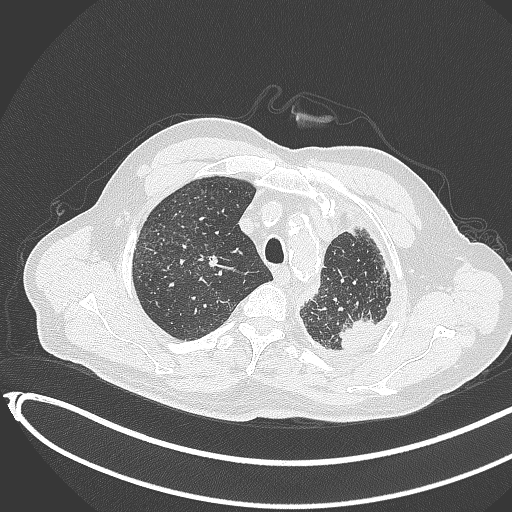
Chest CT, one axial slice; position 353 of 451 along the scan axis; reconstruction kernel B70f; 120 kVp; lung window (W 1500 / L -600 HU); 512 × 512 image matrix. Patient: male, 78 years. Case-level facts recorded for this patient, not image findings: clinical TNM (as recorded): T1c N0 M1.
Structures marked on this image (rectangle marked by the reading radiologist):
- lung tumour (recorded histology: adenocarcinoma): bounding box <335,313,379,355> (left, top, right, bottom; pixels)